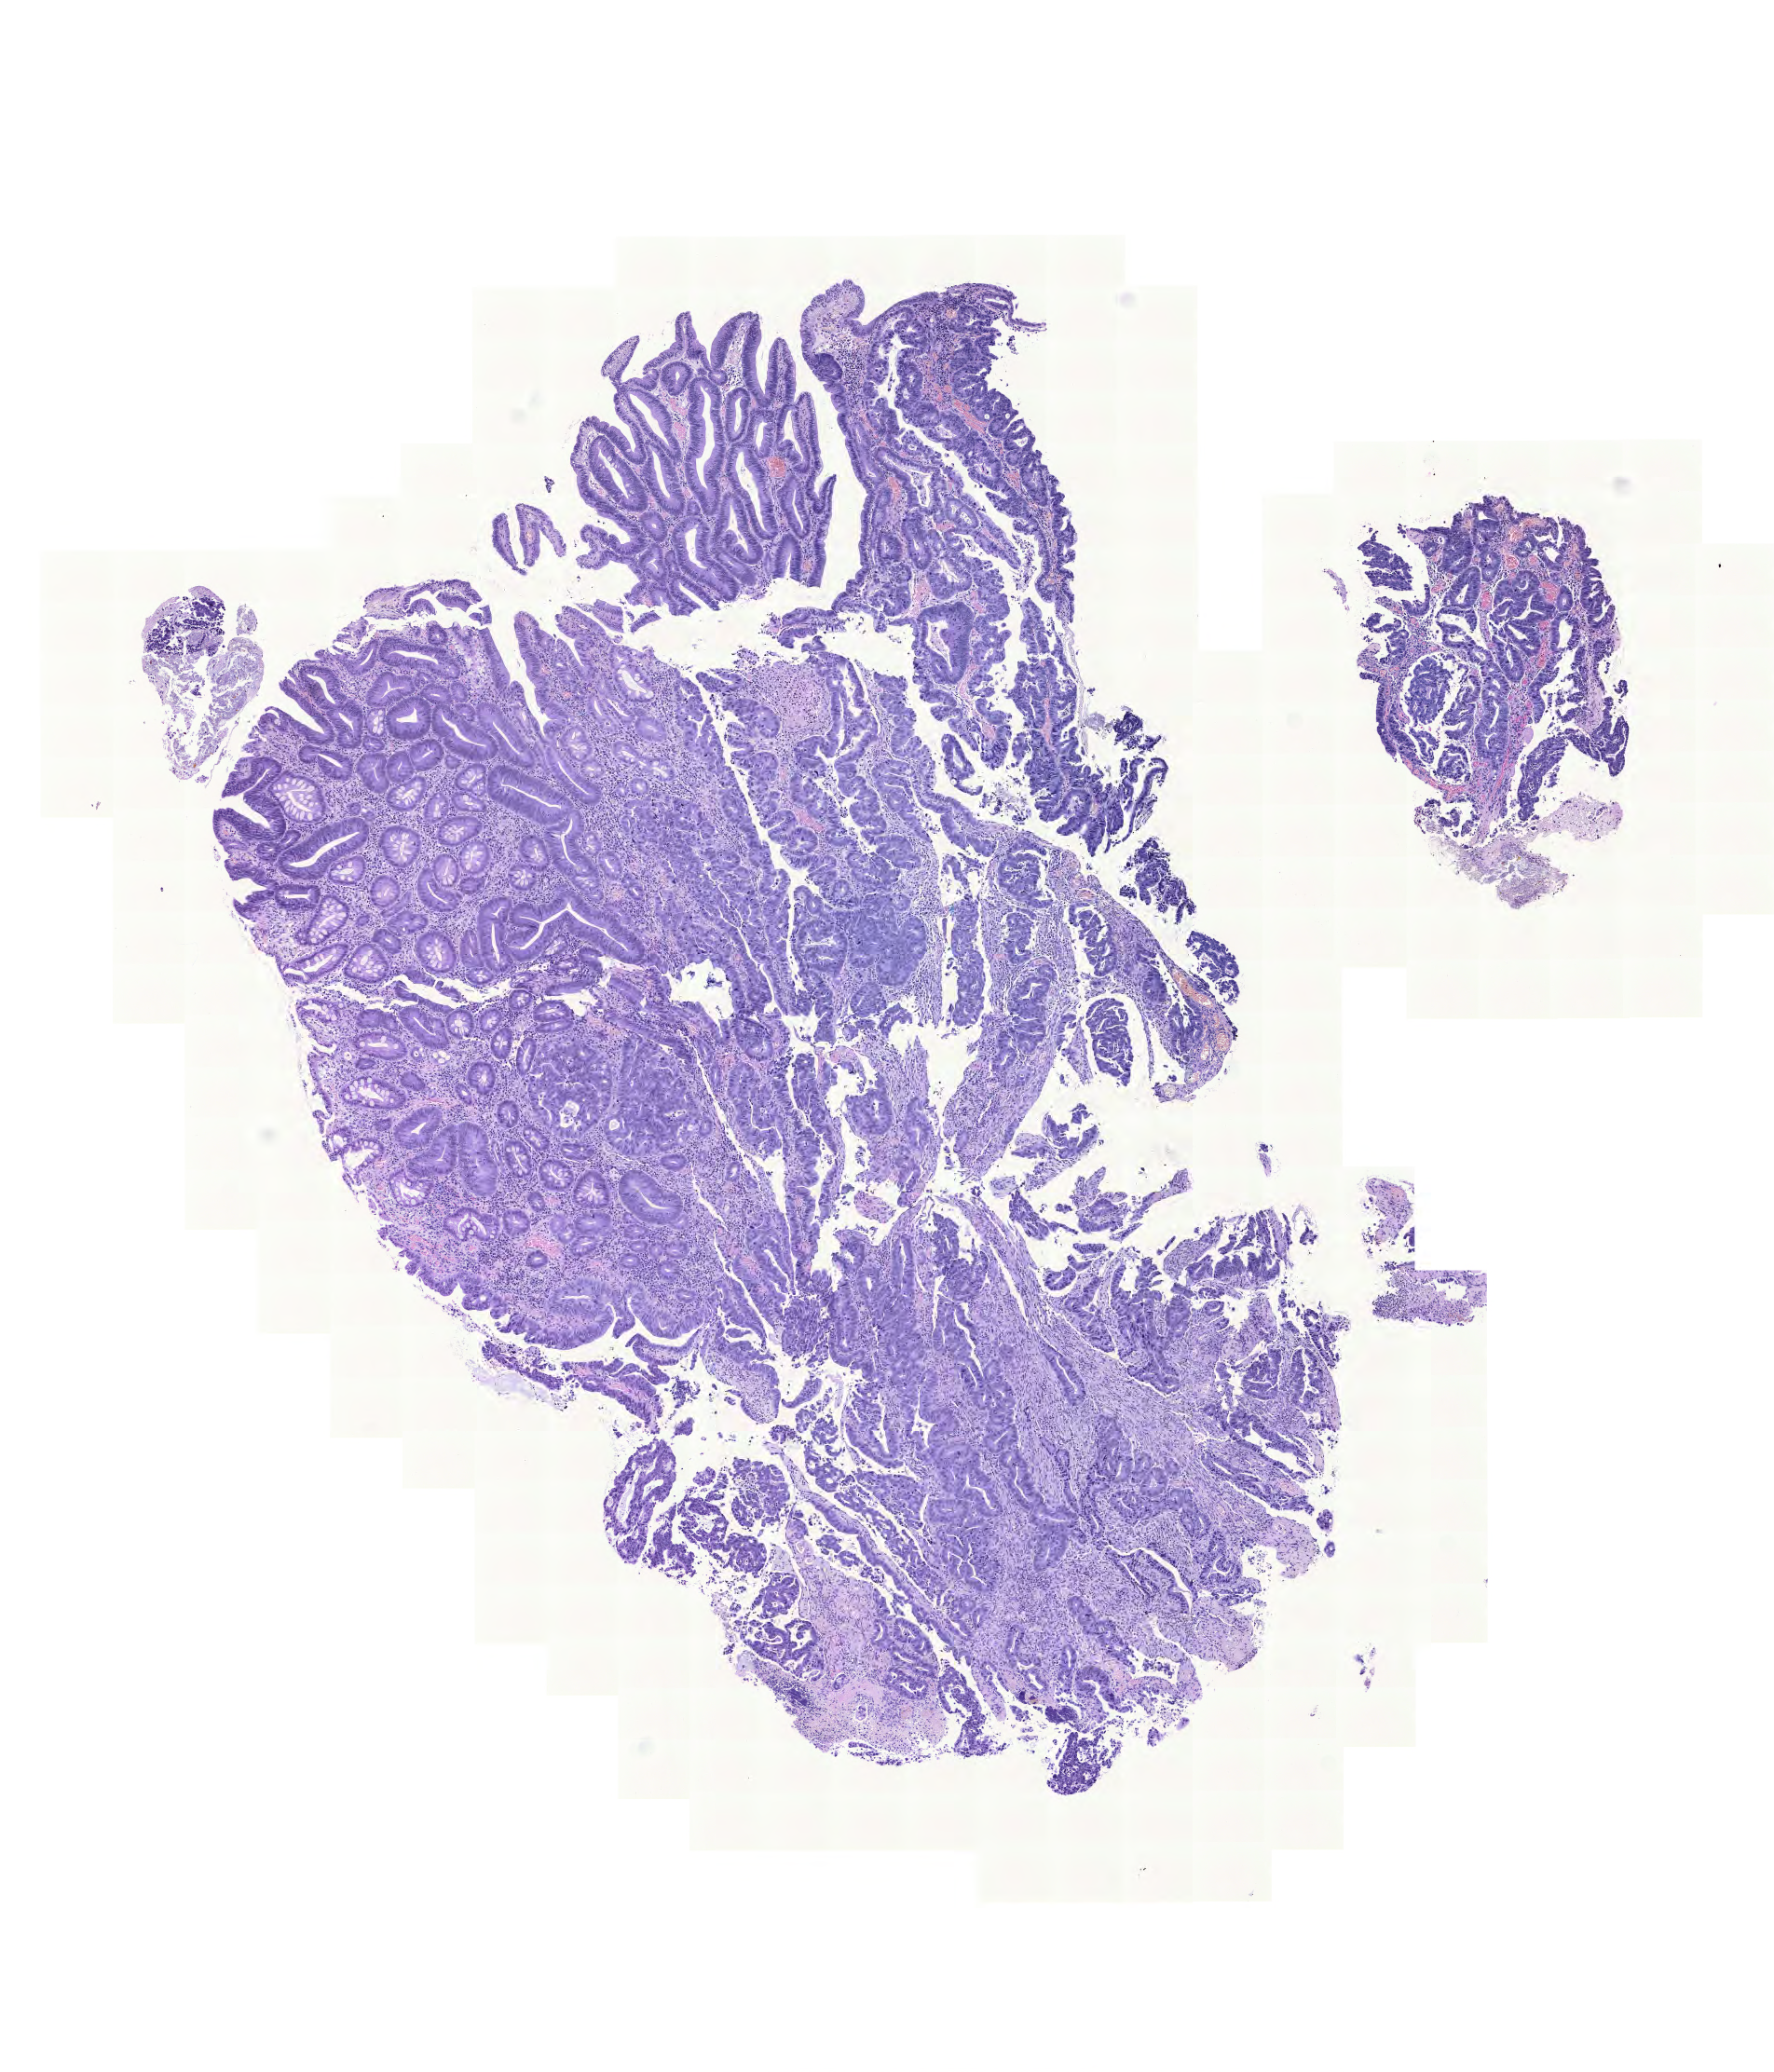
Digitized H&E-stained tissue section (whole slide) — shown as a low-resolution overview of the whole scanned area (about 7.1 x 8.3 mm, from a 20x scan), FFPE section, sample: primary tumour, colon. Female patient; age at initial diagnosis 85 years.
Histologic diagnosis: Adenocarcinoma with mixed subtypes.